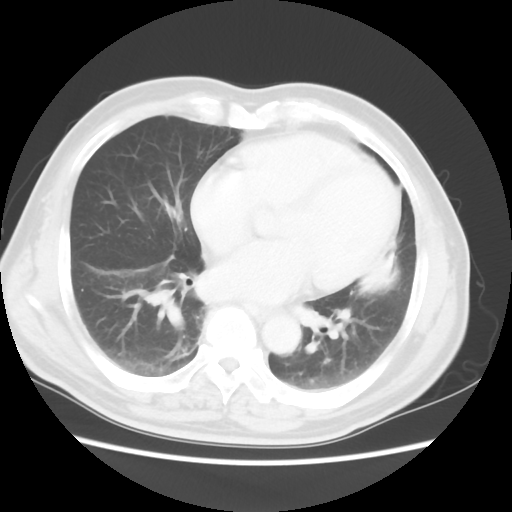
Chest CT, one axial slice; position 20 of 50 along the scan axis; 120 kVp; lung window (W 1500 / L -600 HU); 5 mm slice thickness; 512 × 512 image matrix. Patient: male, 69 years. Case-level facts recorded for this patient, not image findings: clinical TNM (as recorded): T3 N1 M1a.
Annotated regions visible in this slice (bounding box drawn by a radiologist):
- lung tumour (recorded histology: squamous cell carcinoma): bounding box <348,238,403,301> (left, top, right, bottom; pixels)